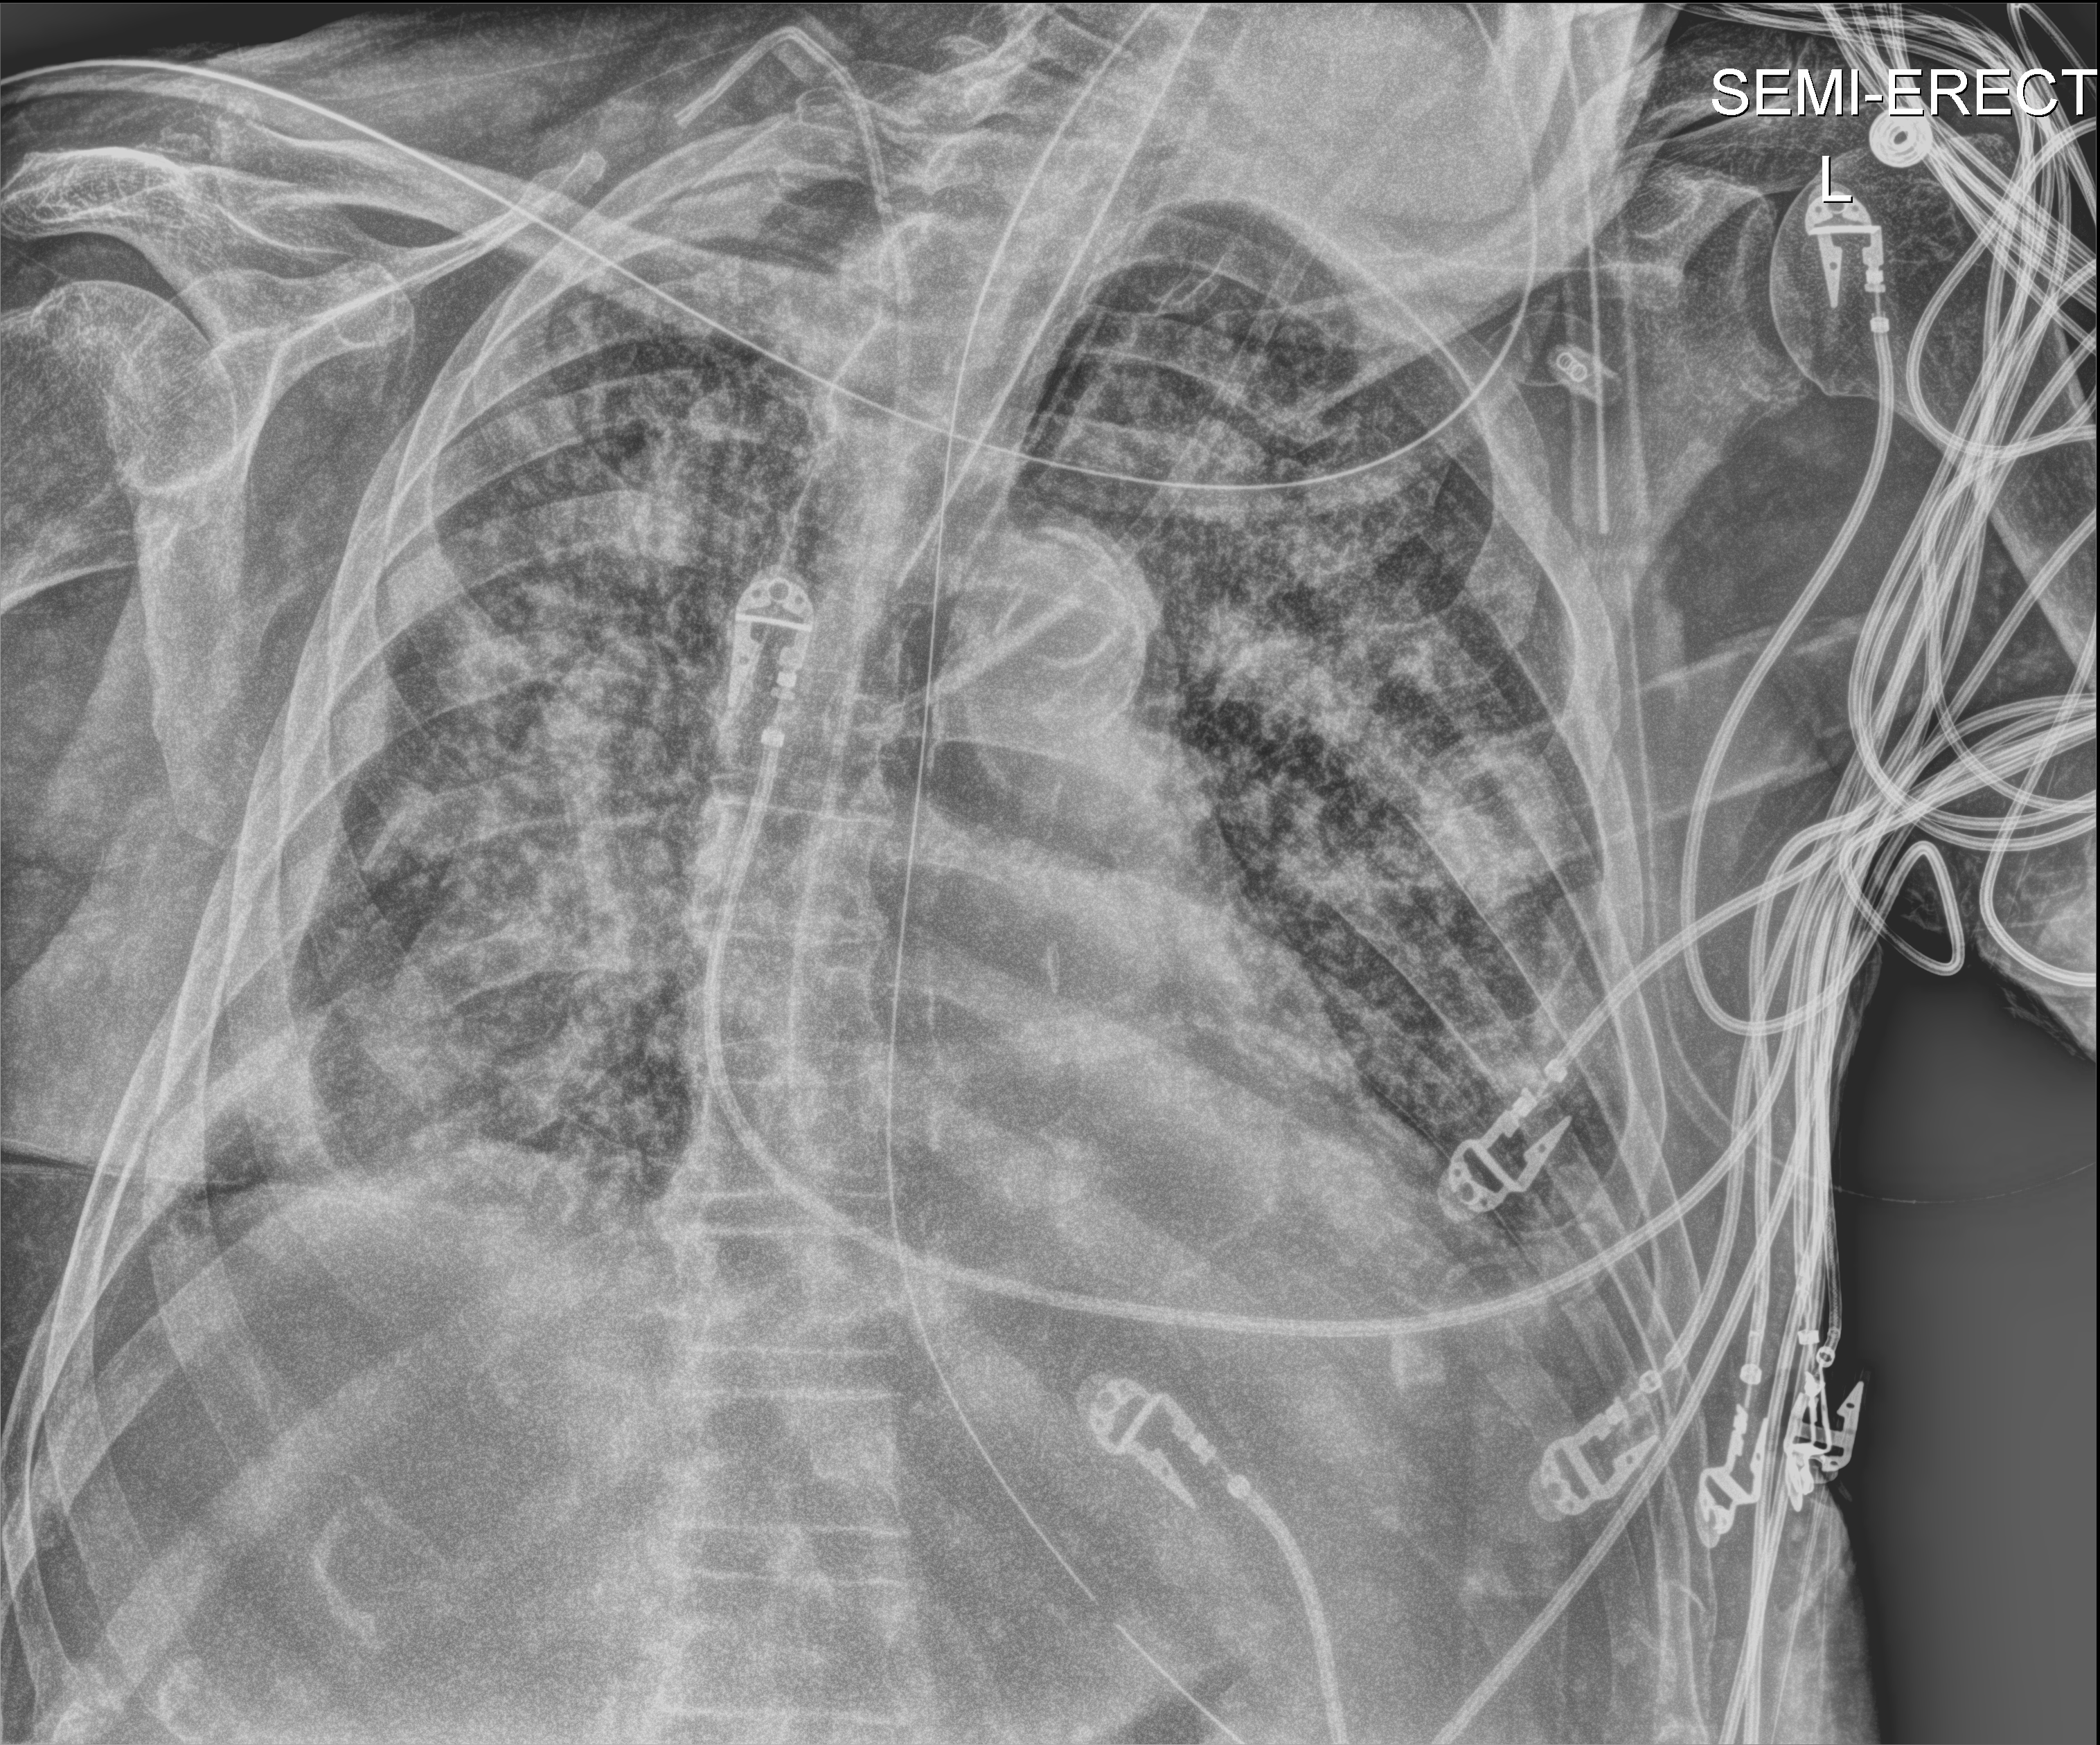
Chest X-ray (portable); anteroposterior (AP) projection. Patient hospitalised with COVID-19; male, aged 75–90 years.
Admission-level facts for this patient (not findings on this image; timing relative to this image not recorded): admitted to intensive care during this hospital stay: yes; mechanically ventilated during this hospital stay: yes.